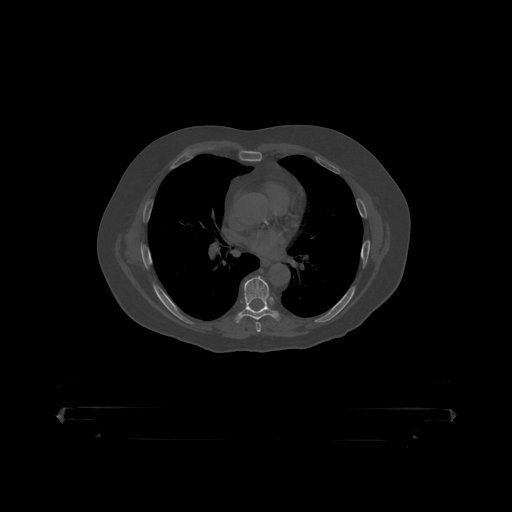
CT including the spine, one axial slice; slice 281 of 390 in the series (ordered by position); reconstruction kernel STANDARD; bone window (W 1800 / L 400 HU); 1.25 mm slice thickness; 512 × 512 image matrix, field of view 650 × 650 mm. Patient: male, 60 years. Case-level facts recorded for this patient, not image findings: primary cancer: prostate.
Structures marked on this image (semi-automatic segmentation, software-assisted and operator-edited):
- T7 vertebra: bounding box (x1, y1, x2, y2) in pixels: (237, 277, 279, 319)